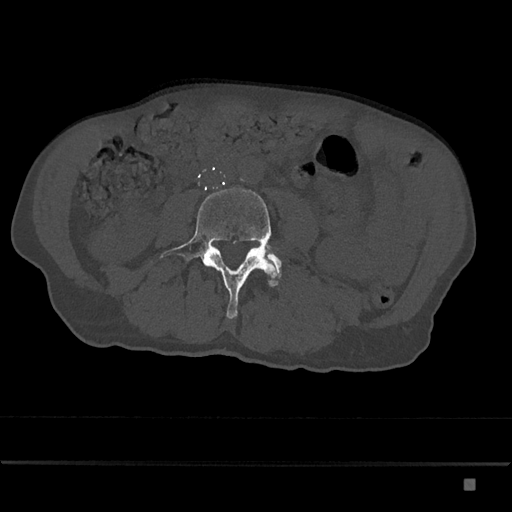
CT including the spine, one axial slice; slice 339 of 797 in the series (ordered by position); bone window (W 1800 / L 400 HU); 0.5 mm slice thickness; 512 × 512 image matrix, field of view 390 × 390 mm. Male patient, age 72 years. From the clinical record (not read from this slice): primary cancer: prostate.
Structures marked on this image (semi-automatic segmentation, software-assisted and operator-edited):
- L4 vertebra: bounding box <160,187,281,319> (left, top, right, bottom; pixels)
- L5 vertebra: <269,254,281,271>